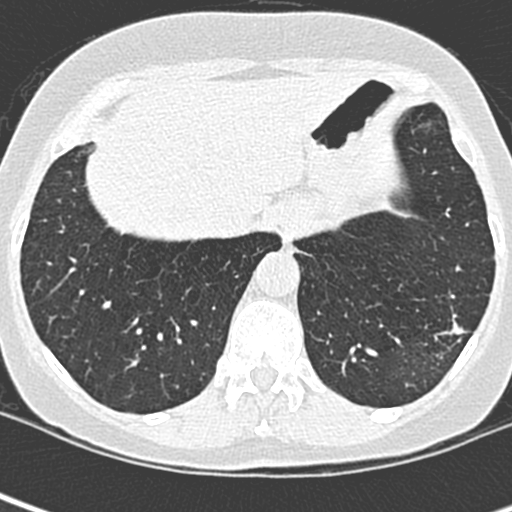
Low-dose screening chest CT, one axial slice. Slice 63 of 252 in the series (ordered by position). Lung window (W 1500 / L -600 HU). 512 × 512 image matrix, field of view 271 × 271 mm.
Annotated regions visible in this slice (expert manual segmentation):
- lesion 1 (tumor, lower lobe of left lung): bounding box (x1, y1, x2, y2) in pixels: (439, 320, 466, 335)